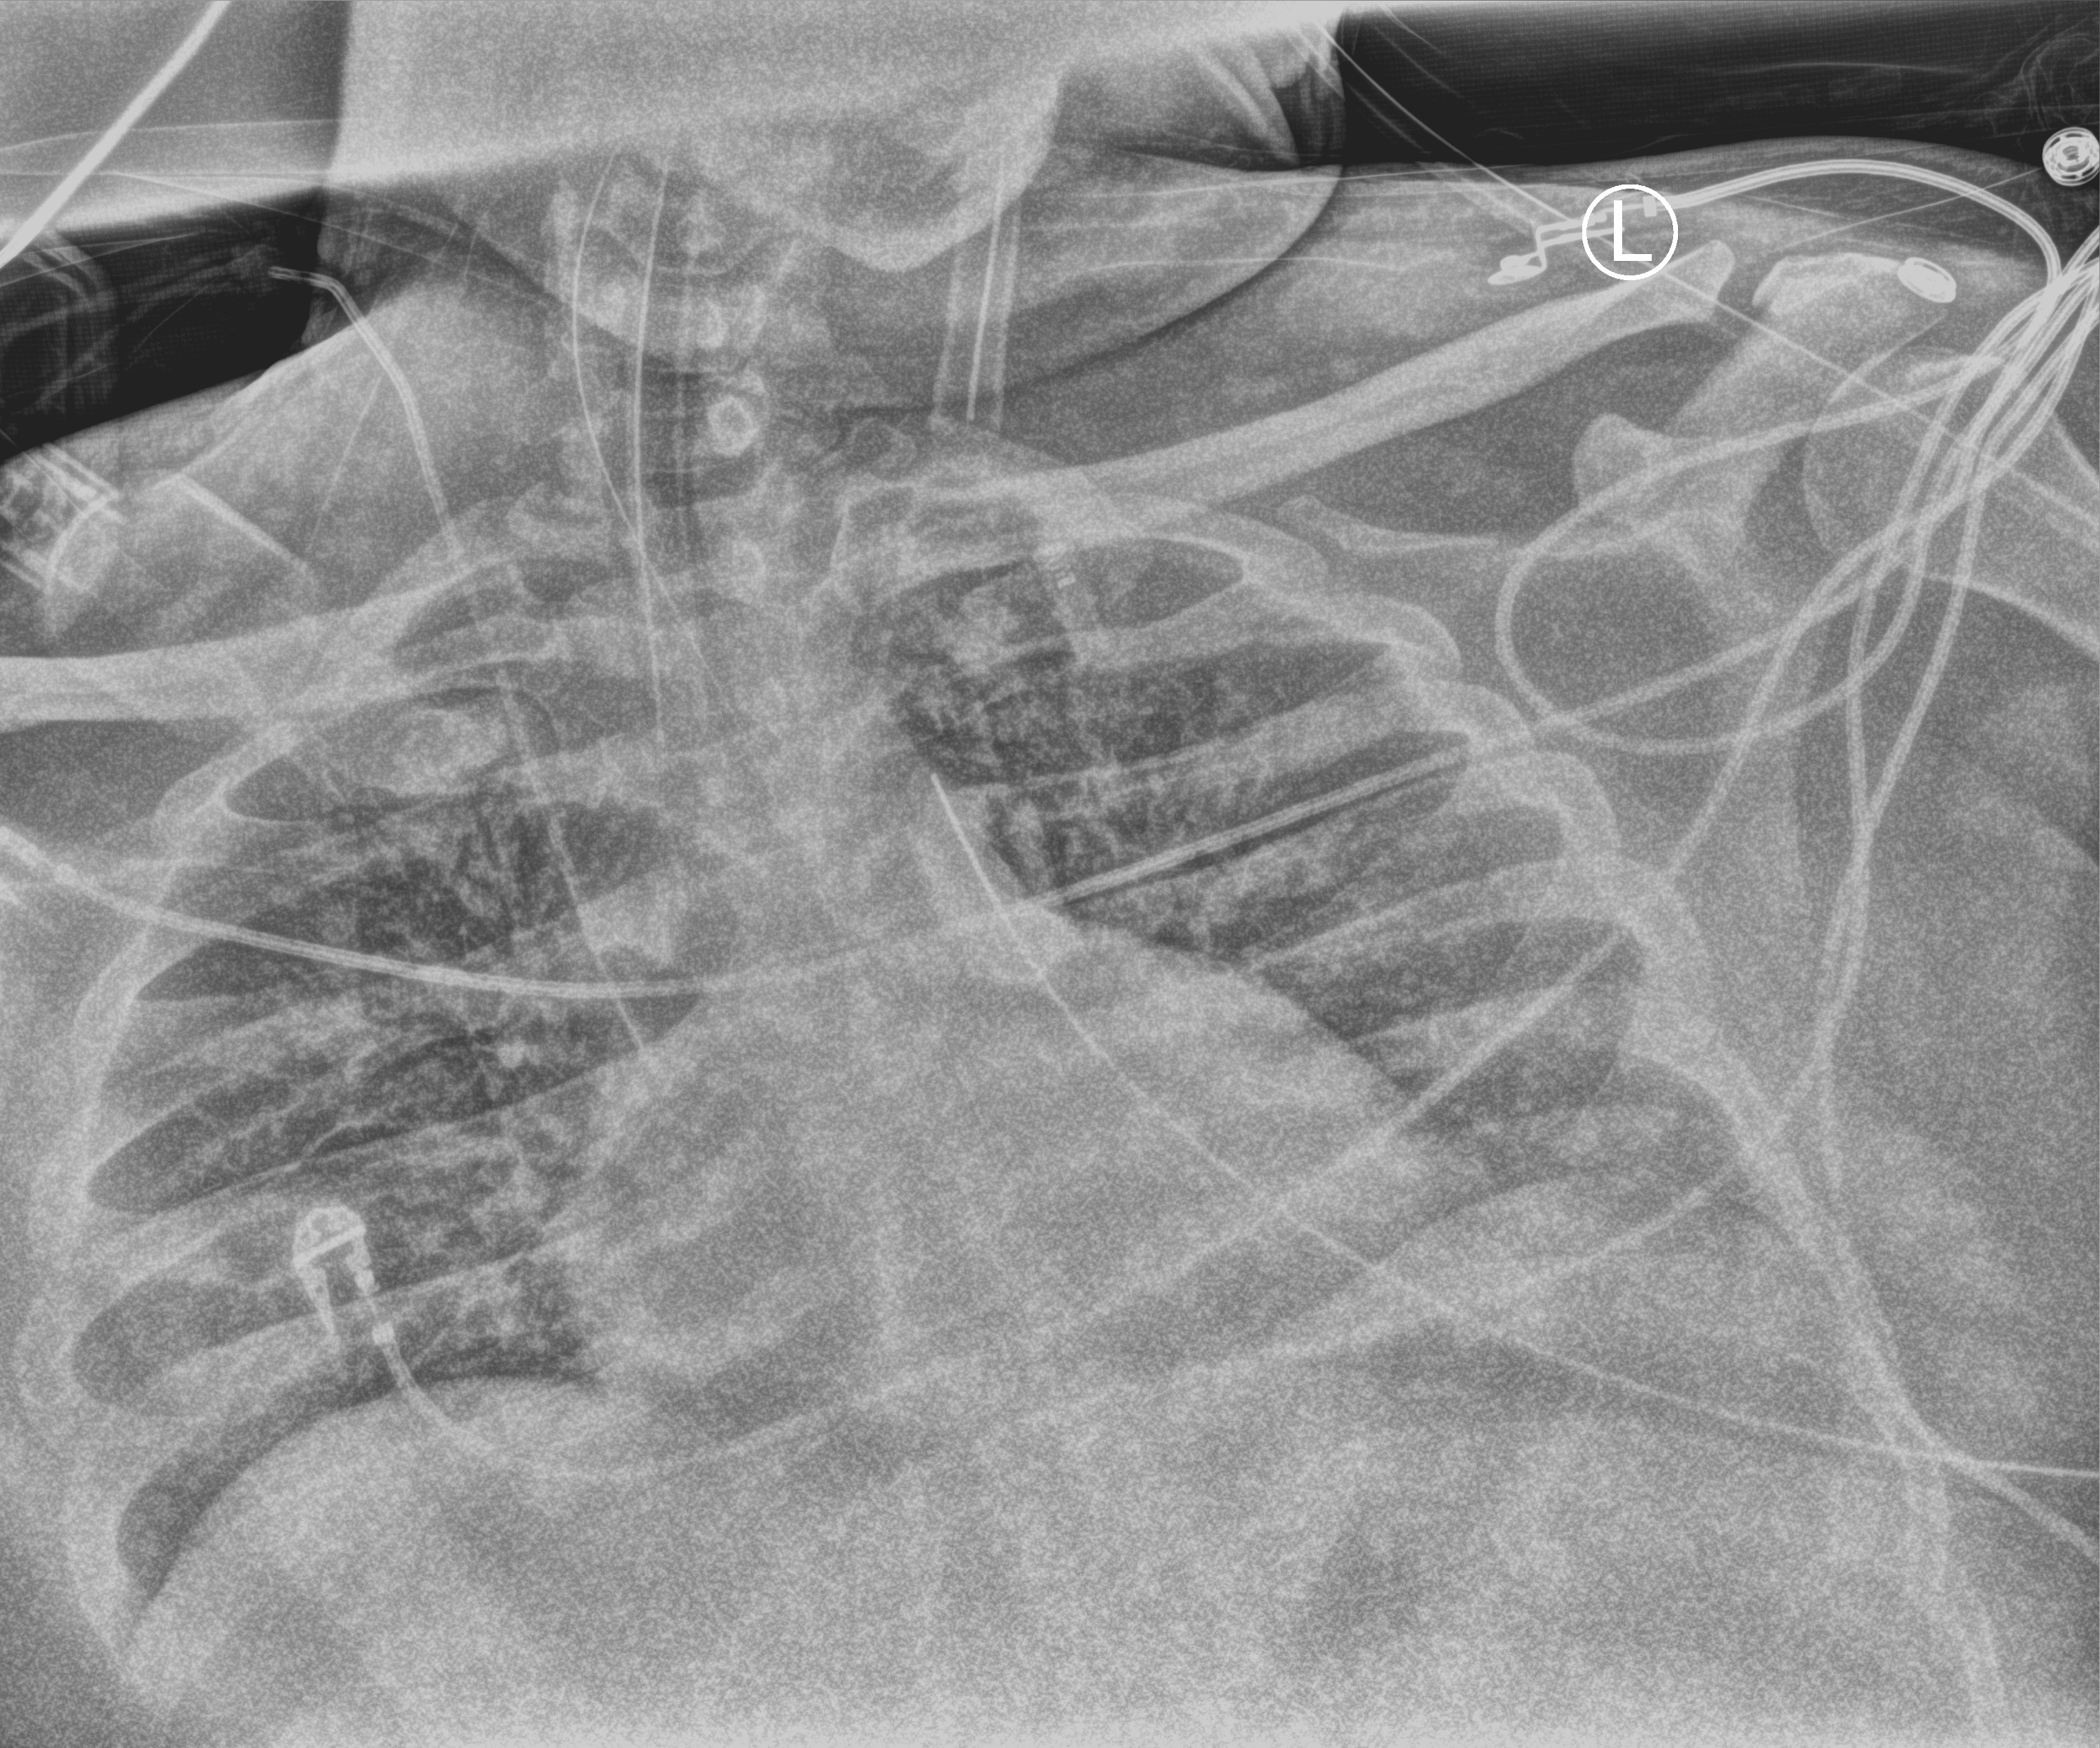
Bedside chest radiograph (computed radiography); anteroposterior (AP) projection. Male patient hospitalised with COVID-19, age 18–59 years.
Admission-level facts for this patient (not findings on this image; timing relative to this image not recorded): mechanically ventilated during this hospital stay: yes; length of hospital stay: 69 days.